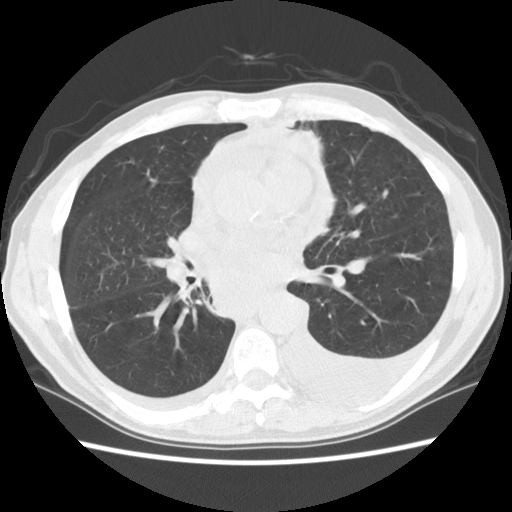
Chest CT (low-dose screening protocol), one axial image. Baseline annual screen. Lung window (W 1500 / L -600 HU). 2.5 mm slice thickness. Slice 59 of 135 in the series. Male, age 60 years at enrolment. Current smoker at enrolment.
Lesion marked by an expert reader, bounding box [x1, y1, x2, y2] px = [174, 240, 304, 332]. Screening reader's record for this exam: no non-calcified nodule ≥4 mm recorded.